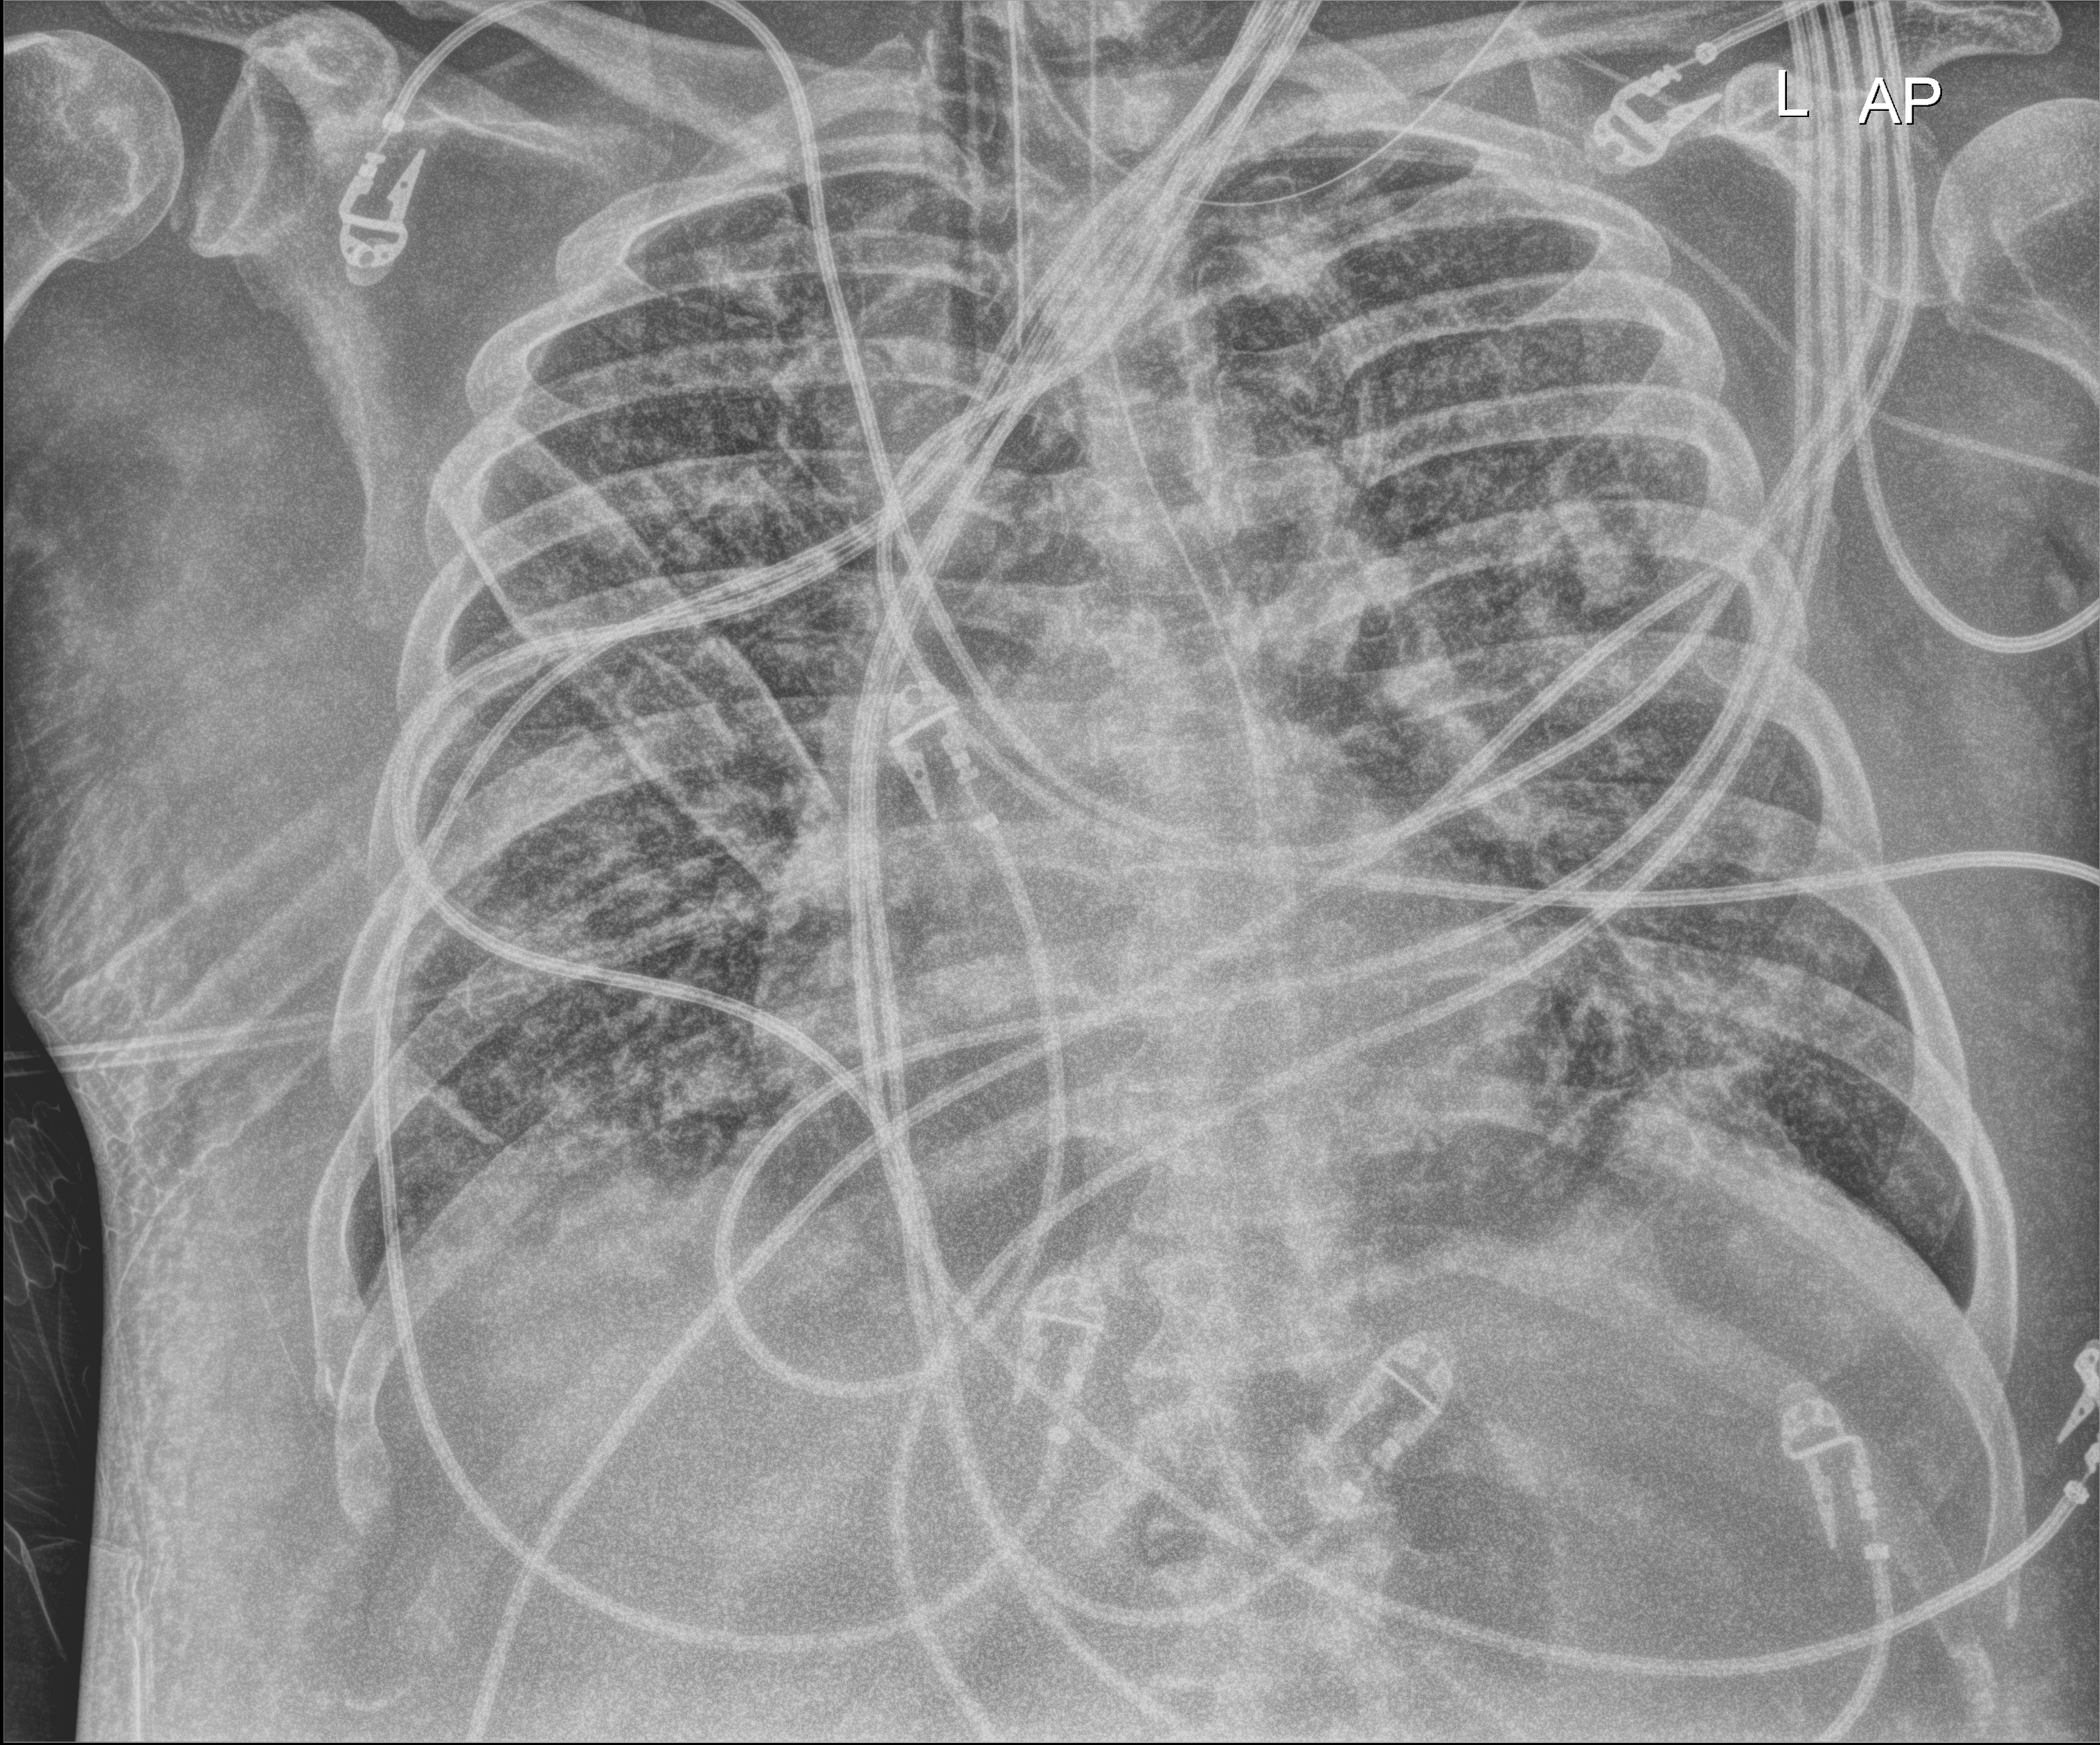
Bedside chest radiograph (digital radiography), anteroposterior (AP) projection. Patient hospitalised with COVID-19; male, aged 60–74 years.
Hospital-stay facts (about this admission, not read from this image; timing relative to this image not recorded): mechanically ventilated during this hospital stay: yes; admitted to intensive care during this hospital stay: yes; chronic kidney disease (admission record): no.